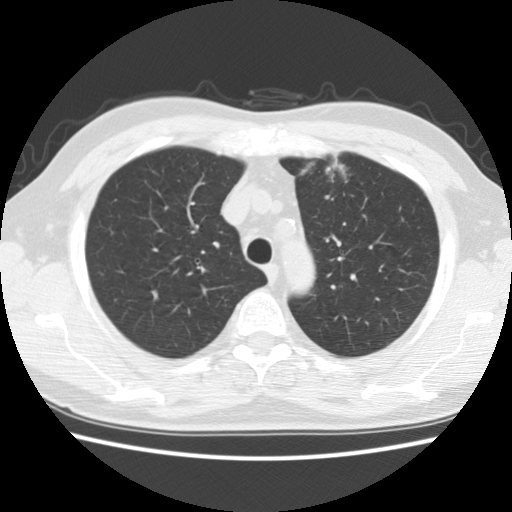
Chest CT (low-dose screening protocol), one axial image, second screening round (one year after baseline), lung window (W 1500 / L -600 HU), 2.5 mm slice thickness, slice 42 of 172 in the series. Male participant, aged 63 years at enrolment. Former smoker at enrolment.
Expert reader's lesion annotation, bounding box (x1, y1, x2, y2) in pixels: (297, 147, 359, 206). Reader record for this screening exam (exam-level; its link to the box is not recorded): non-calcified nodule or mass ≥4 mm, left upper lobe, 23 × 18 mm, spiculated (stellate) margins, soft tissue attenuation, pre-existing on the prior screen: yes; interval growth: yes. Official screen result: positive, other. Later outcome: lung cancer diagnosed 83 days after this screen — adenocarcinoma, NOS, left upper lobe, moderately differentiated (G2), stage IA (AJCC 6th edition), 14 mm at pathology.